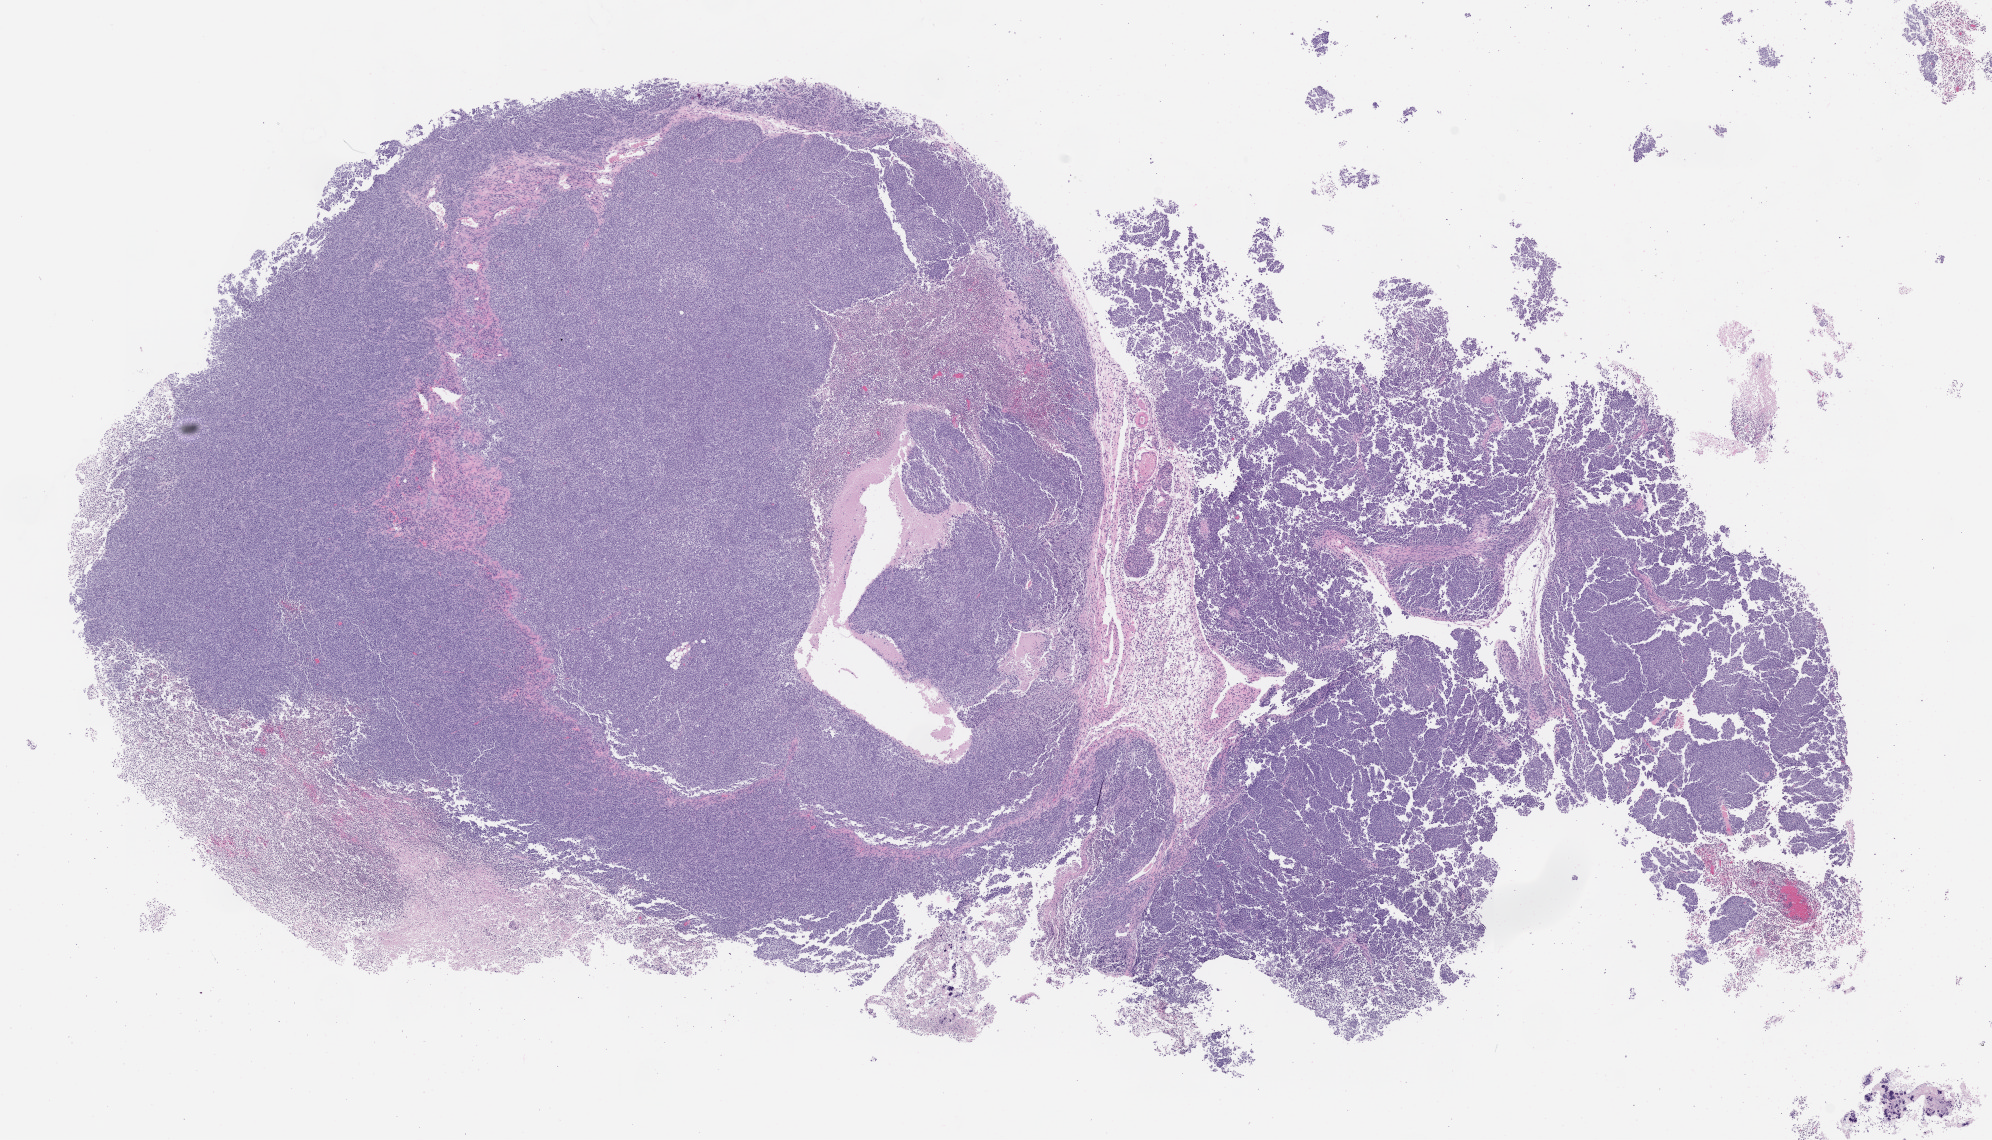
Whole-slide image, H&E: patient-derived xenograft (human tumor grown in a mouse), passage 1, whole scanned area (about 16.0 x 9.2 mm) shown as a low-resolution overview, FFPE section, originating tumor site category: musculoskeletal.
* originating patient diagnosis: Ewing Sarcoma|Primitive Neuroectodermal Tumor